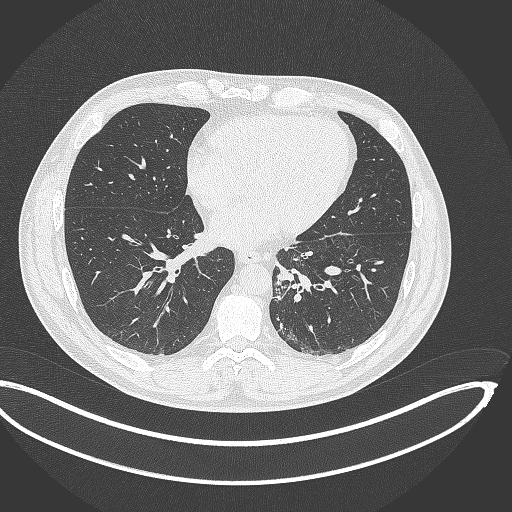
Chest CT, one axial slice; slice 131 of 362 in the series (ordered by position); lung window (W 1500 / L -600 HU); 1 mm slice thickness; 512 × 512 image matrix, field of view 442 × 442 mm. Patient: male, 50 years. From the clinical record (not read from this slice): clinical TNM (as recorded): T2a N3 M0.
Annotated regions visible in this slice (bounding box drawn by a radiologist):
- lung tumour (recorded histology: squamous cell carcinoma): bounding box <273,273,294,305> (left, top, right, bottom; pixels)